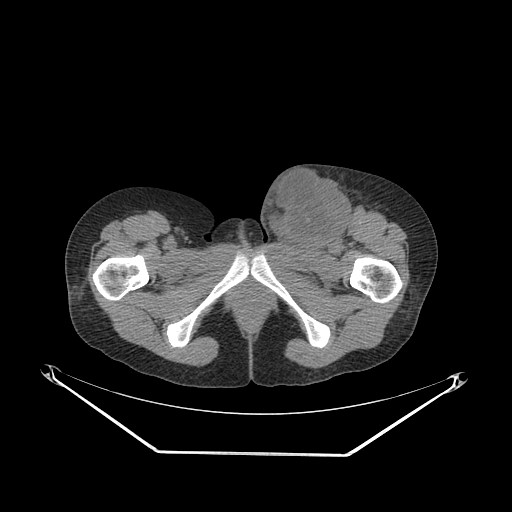
CT of an extremity soft-tissue mass (from a PET/CT study), one axial slice; position 57 of 267 along the scan axis; 140 kVp; soft-tissue window (W 400 / L 40 HU); 512 × 512 image matrix, field of view 500 × 500 mm. Female patient. From the clinical record (not read from this slice): histological type: leiomyosarcoma; grade: high; site of the primary tumour: groin.
Annotated regions visible in this slice (expert contour drawn on MRI and transferred to this co-registered scan by the dataset authors):
- gross tumour volume including surrounding oedema: bounding box [x1, y1, x2, y2] px = [256, 164, 369, 250]
- gross tumour volume (mass): [265, 169, 350, 247]